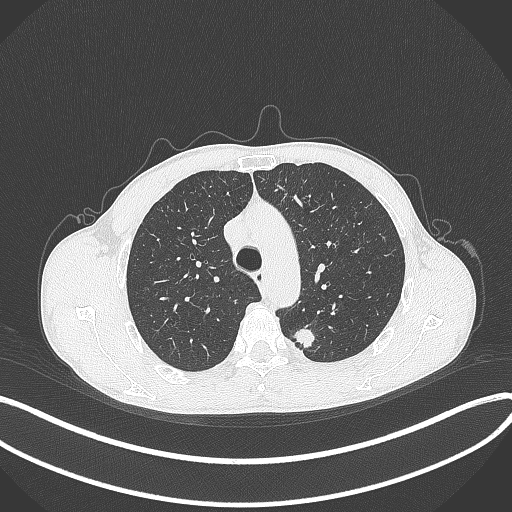
Chest CT, one axial slice; position 295 of 429 along the scan axis; reconstruction kernel B70f; 120 kVp; lung window (W 1500 / L -600 HU); 1 mm slice thickness; 512 × 512 image matrix, field of view 400 × 400 mm. Male patient, age 51 years. Case-level facts recorded for this patient, not image findings: clinical TNM (as recorded): T2a N1 M1.
Structures marked on this image (bounding box drawn by a radiologist):
- lung tumour (recorded histology: adenocarcinoma): bounding box <291,323,320,352> (left, top, right, bottom; pixels)